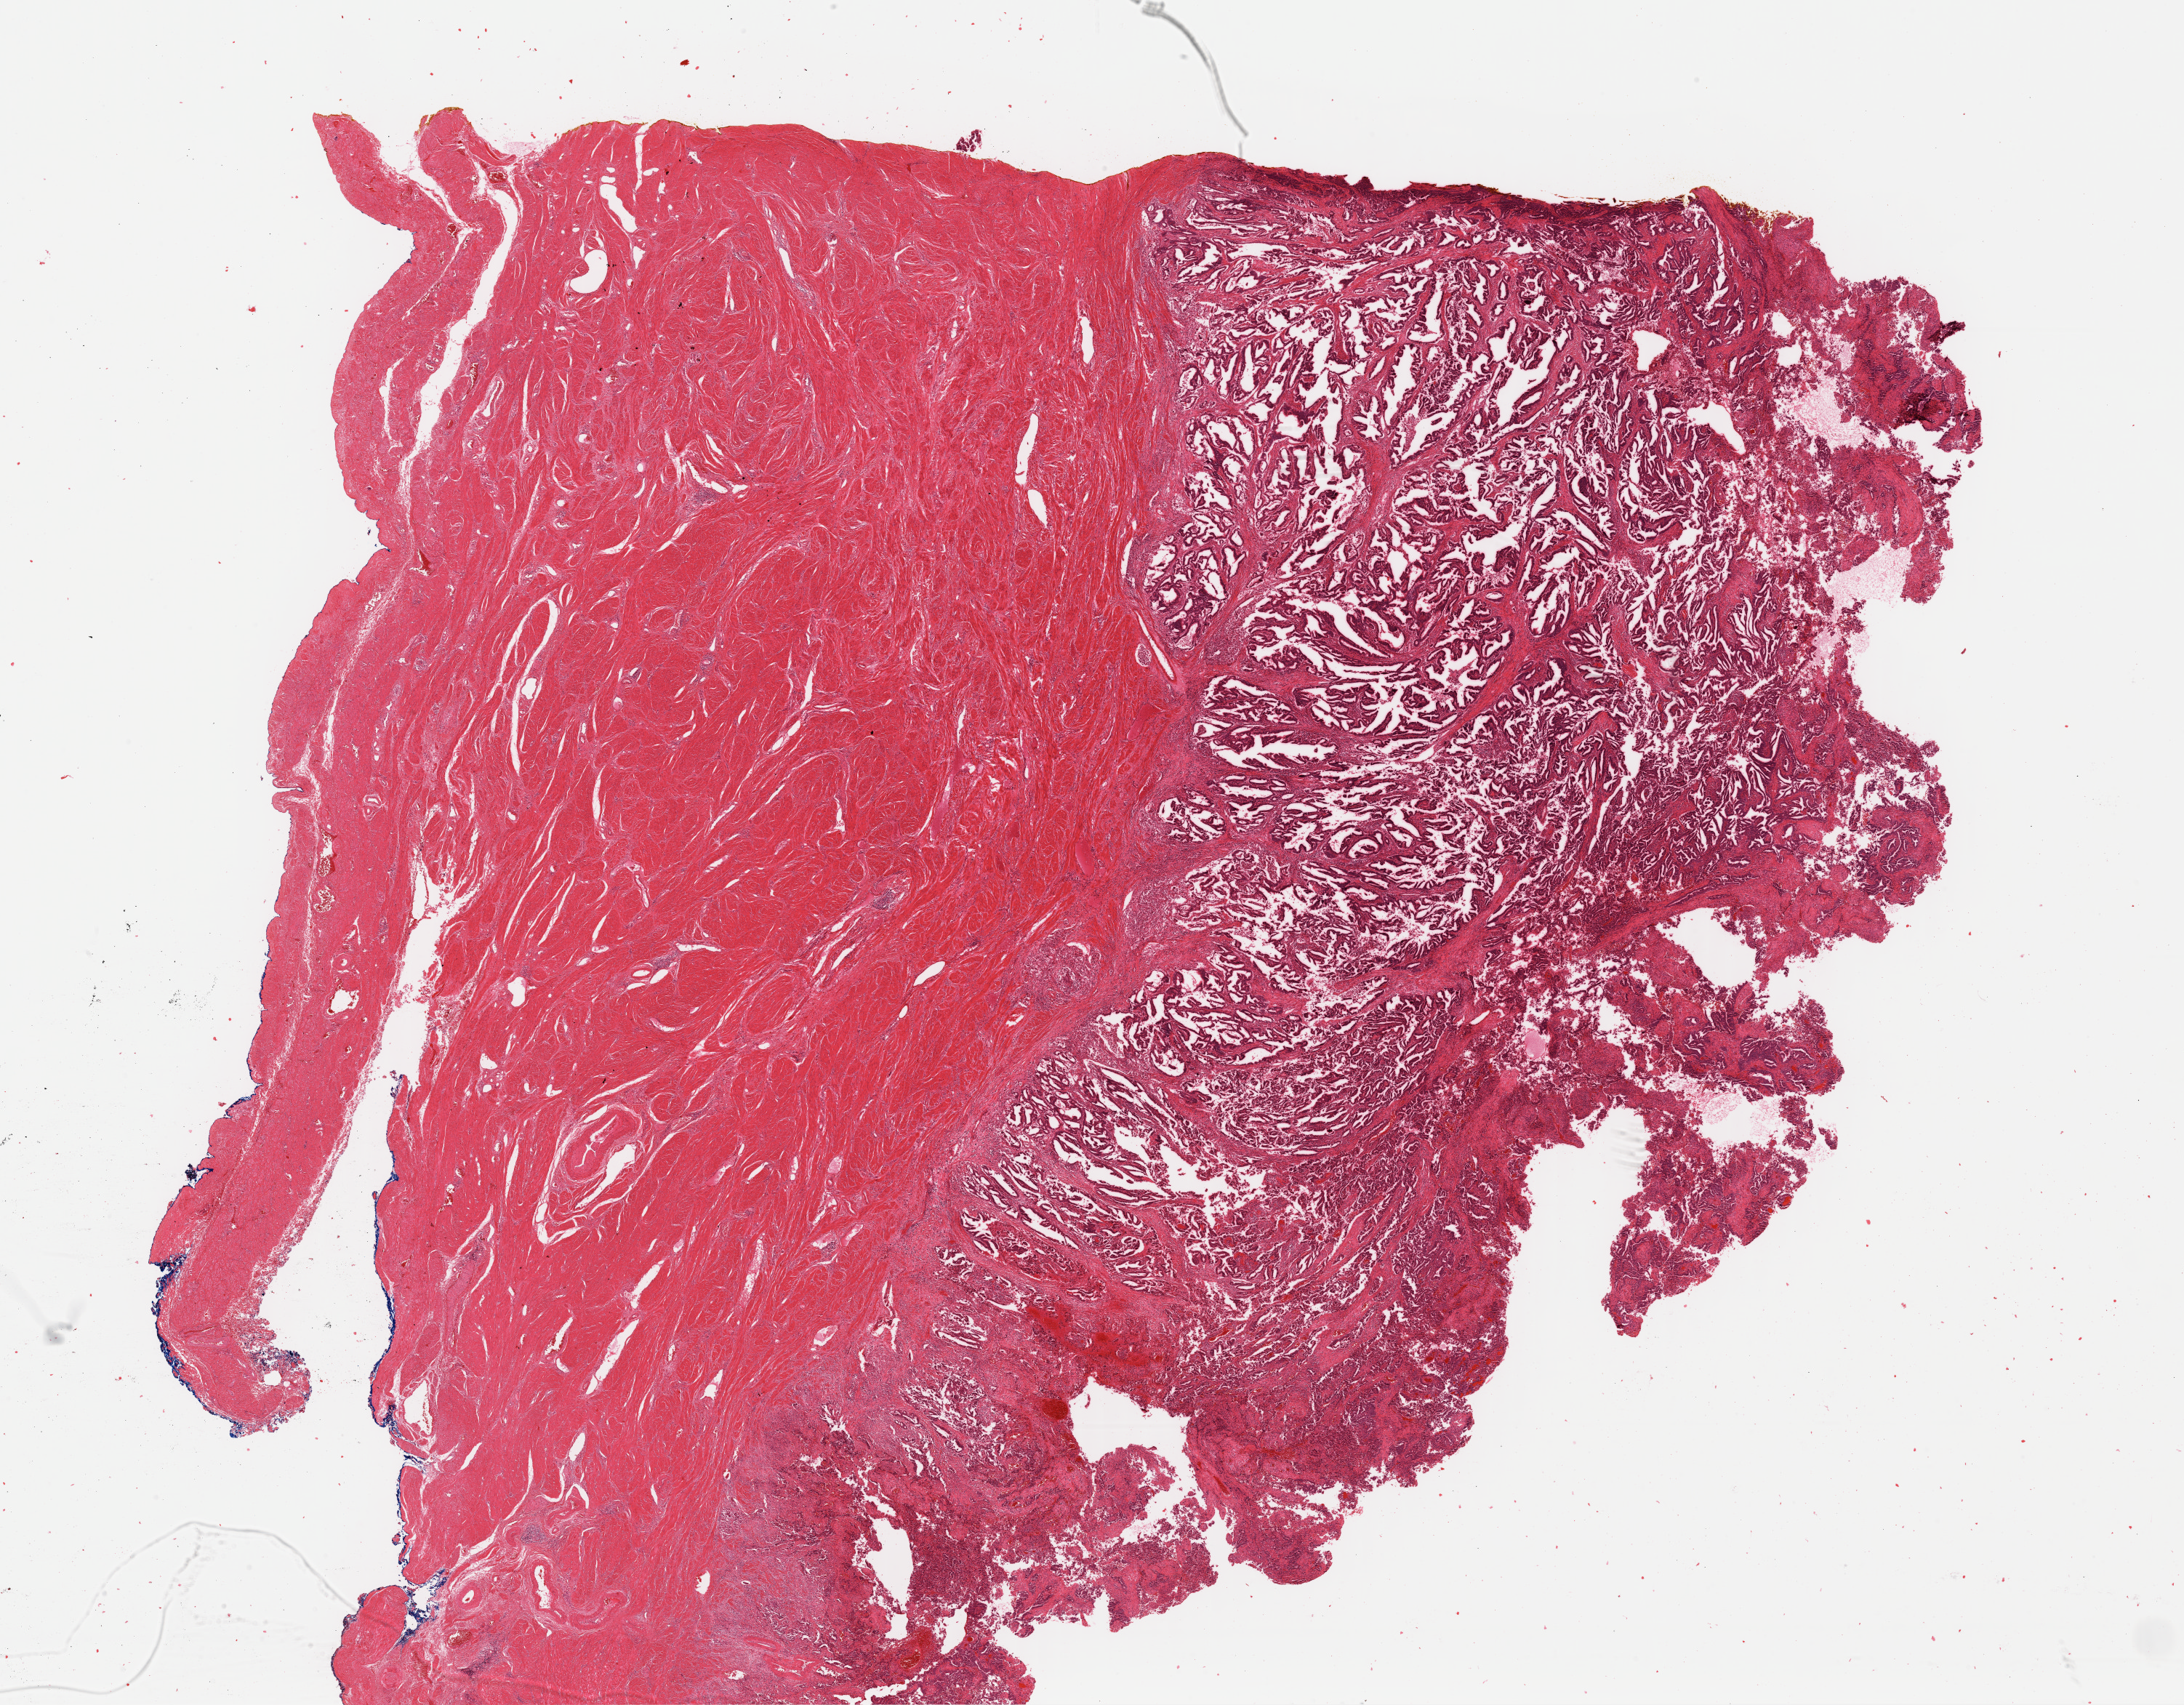
Digitized H&E-stained tissue section (whole slide), whole scanned area (about 23.7 x 18.5 mm, acquisition: 40x scan) shown as a low-resolution overview; FFPE section; sample: primary tumour, uterus. Female patient; age at initial diagnosis 37 years. Histologic grade: G2 (moderately differentiated).
* FIGO stage: IIIA
* pathologic diagnosis: Endometrioid adenocarcinoma, NOS (endometrium)